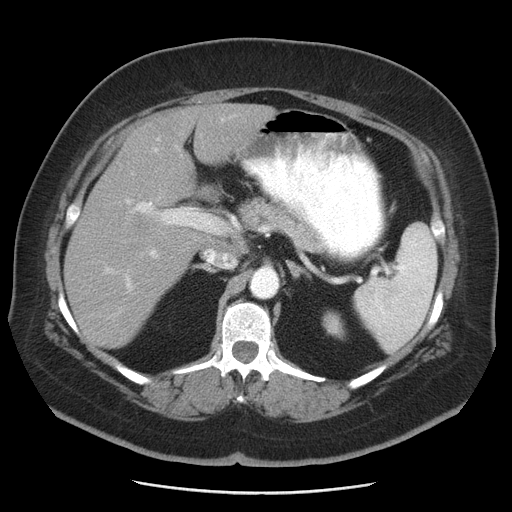
Contrast-enhanced abdominal CT, one axial slice; slice 29 of 55 in the series (ordered by position); reconstruction kernel STANDARD; intravenous contrast given; soft-tissue window (W 400 / L 40 HU); 5 mm slice thickness; 512 × 512 image matrix, field of view 380 × 380 mm. Female patient, age 52 years. Case-level facts recorded for this patient, not image findings: diagnosis: colorectal cancer liver metastases, imaged before liver resection; multiple liver metastases: yes; largest metastasis: 2.5 cm; disease in both lobes: yes.
Structures marked on this image (outlined manually by an expert reader):
- liver: bounding box <64,103,274,348> (left, top, right, bottom; pixels)
- planned liver remnant (the part of the liver to remain after resection): <64,194,209,348>
- portal vein (with intrahepatic branches): <103,138,221,289>